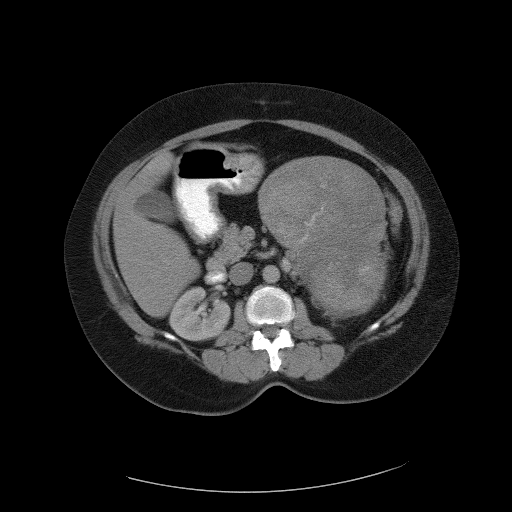
Contrast-enhanced abdominal CT, one axial slice; position 60 of 90 along the scan axis; reconstruction kernel FC01; 120 kVp; intravenous contrast given; soft-tissue window (W 400 / L 40 HU); 5 mm slice thickness; 512 × 512 image matrix. Patient: female, 55 years. Case-level facts recorded for this patient, not image findings: diagnosis: adrenocortical carcinoma; tumour side: left adrenal; tumour size at pathology: 22 cm; Ki-67 index: 10 %; stage (as recorded): 3.
Annotated regions visible in this slice (semi-automatic segmentation, software-assisted and operator-edited):
- mass: box from (x=261, y=157) to (x=386, y=316) px